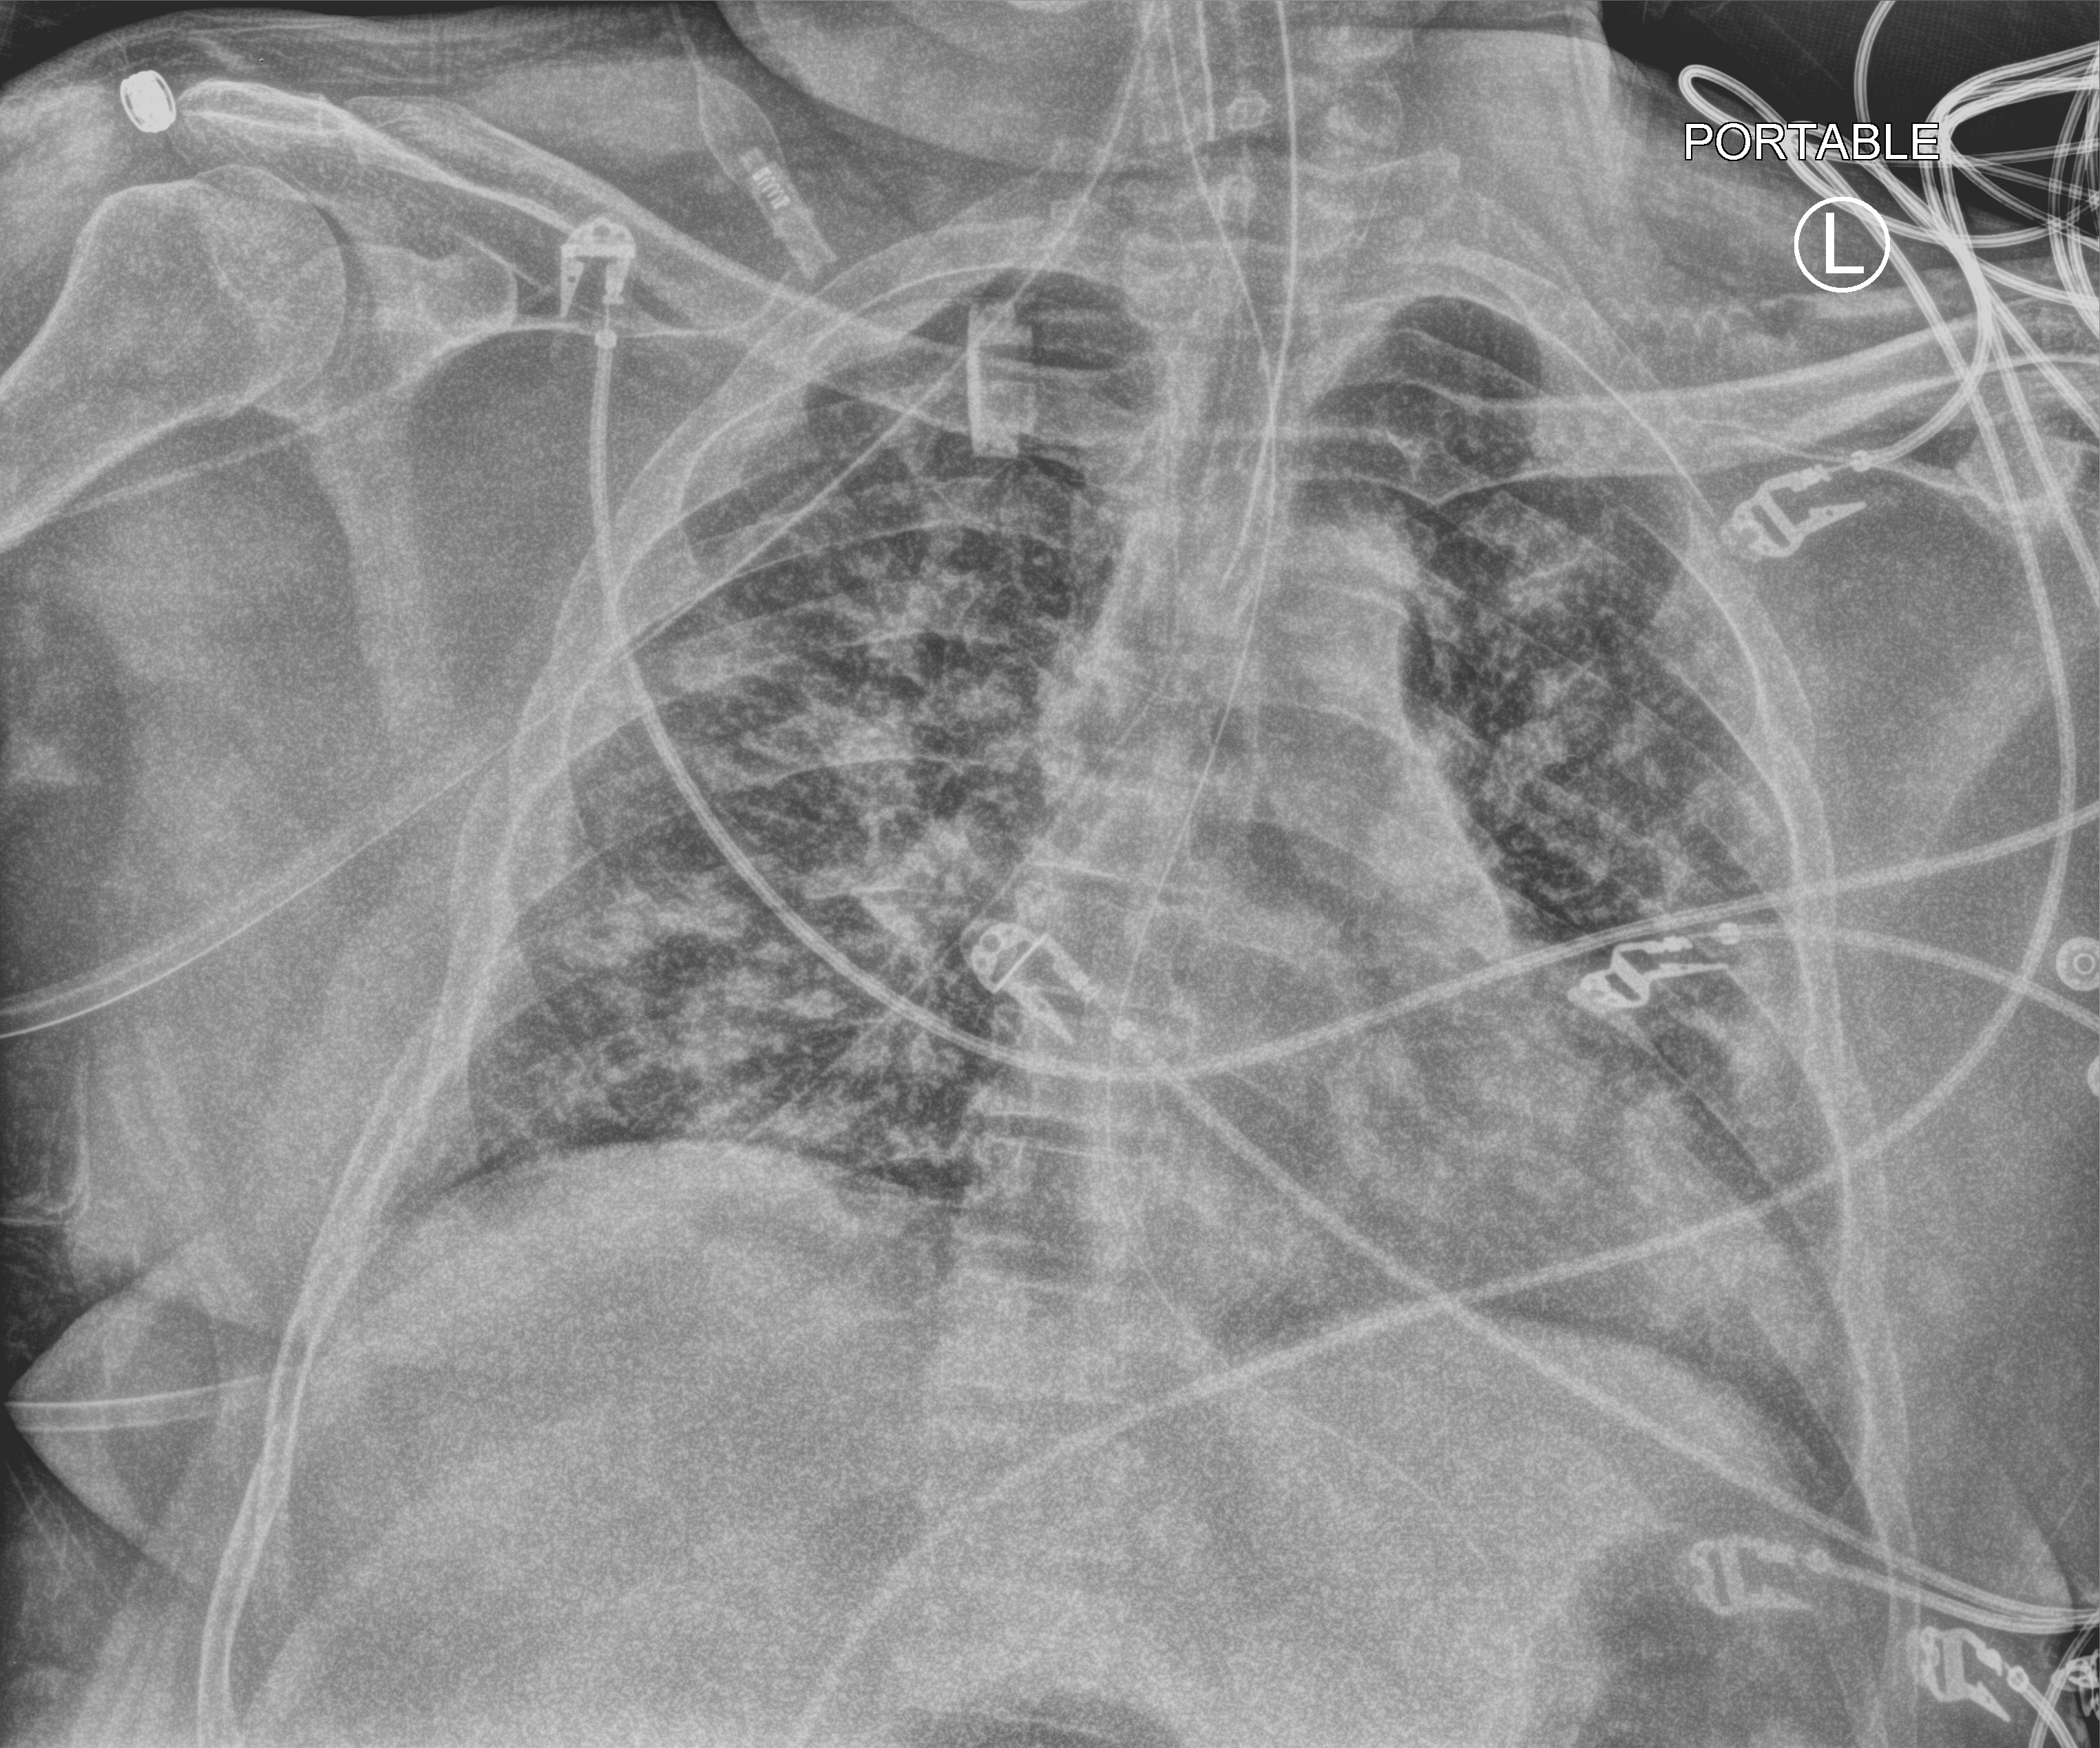
Chest X-ray (portable); anteroposterior (AP) projection. Male patient hospitalised with COVID-19, age 18–59 years.
Hospital-stay facts (about this admission, not read from this image; timing relative to this image not recorded):
- mechanically ventilated during this hospital stay: yes
- diabetes (admission record): no